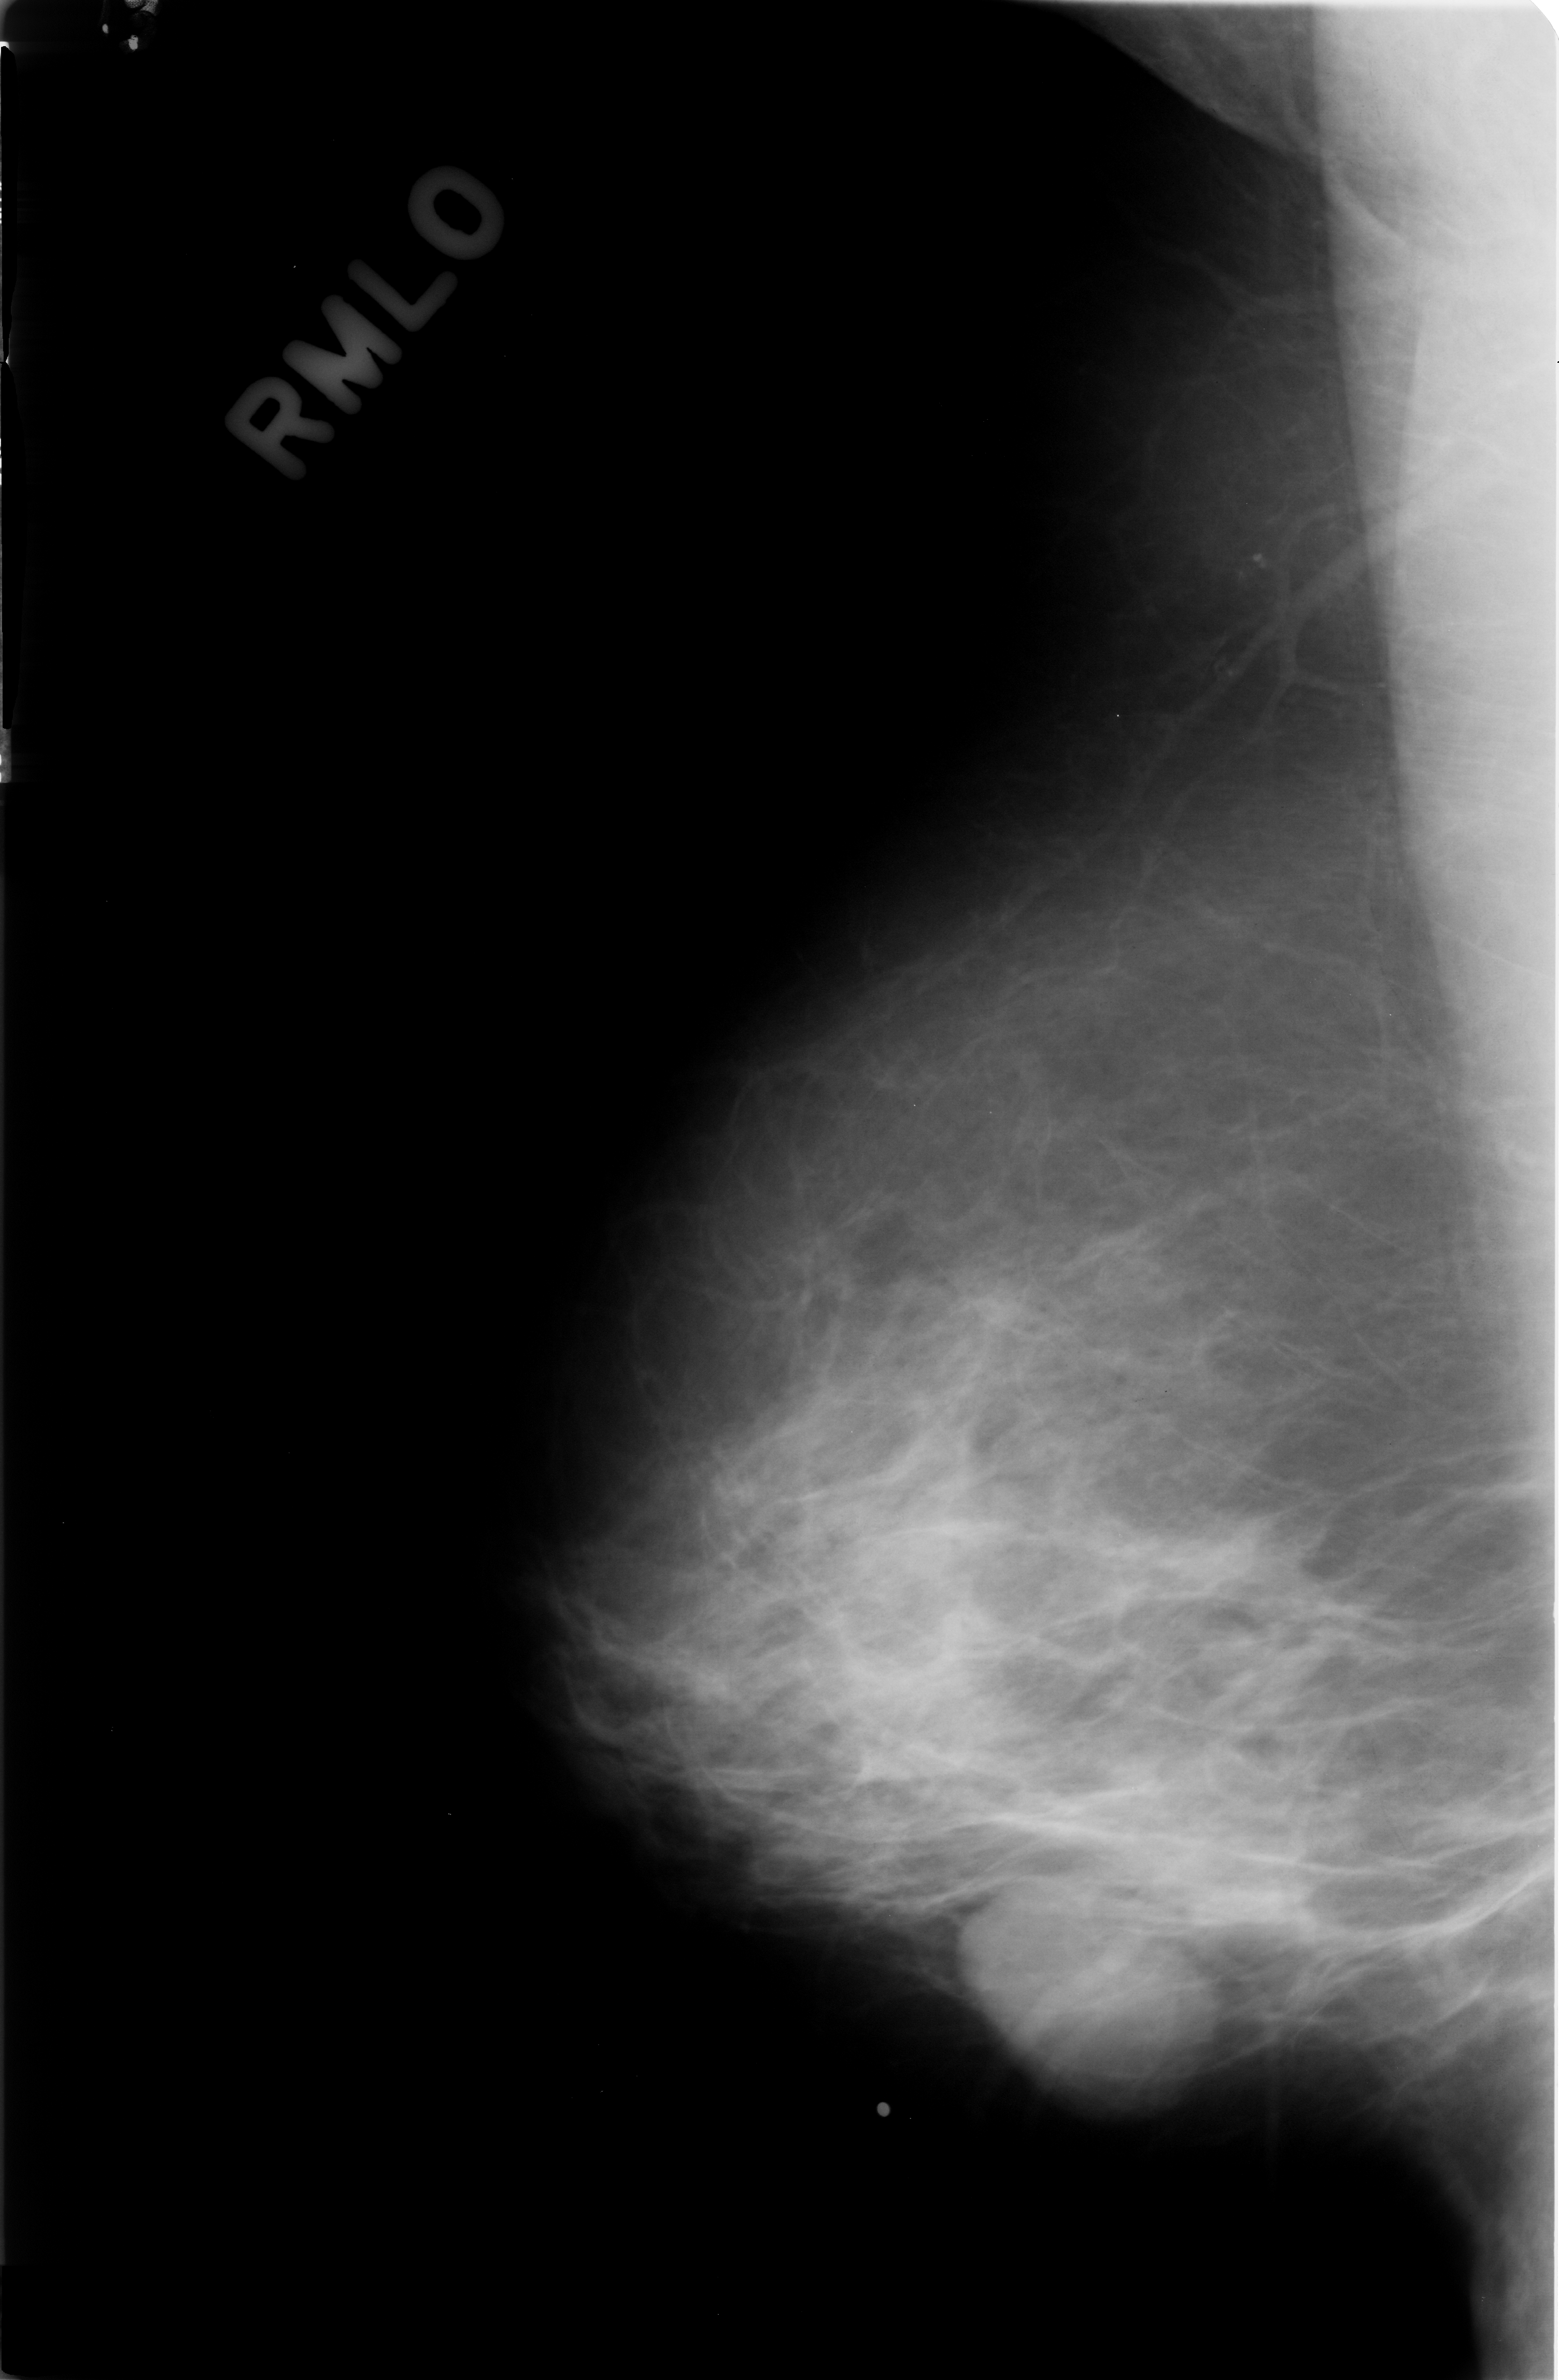
Mammogram (digitized film), right breast, MLO view, breast composition: scattered fibroglandular densities (BI-RADS density category 2 of 4).
Finding: mass, shape oval, margins circumscribed; BI-RADS assessment category 3; subtlety rating 5 on a 1 (subtle) to 5 (obvious) scale; pathology (as recorded): benign.